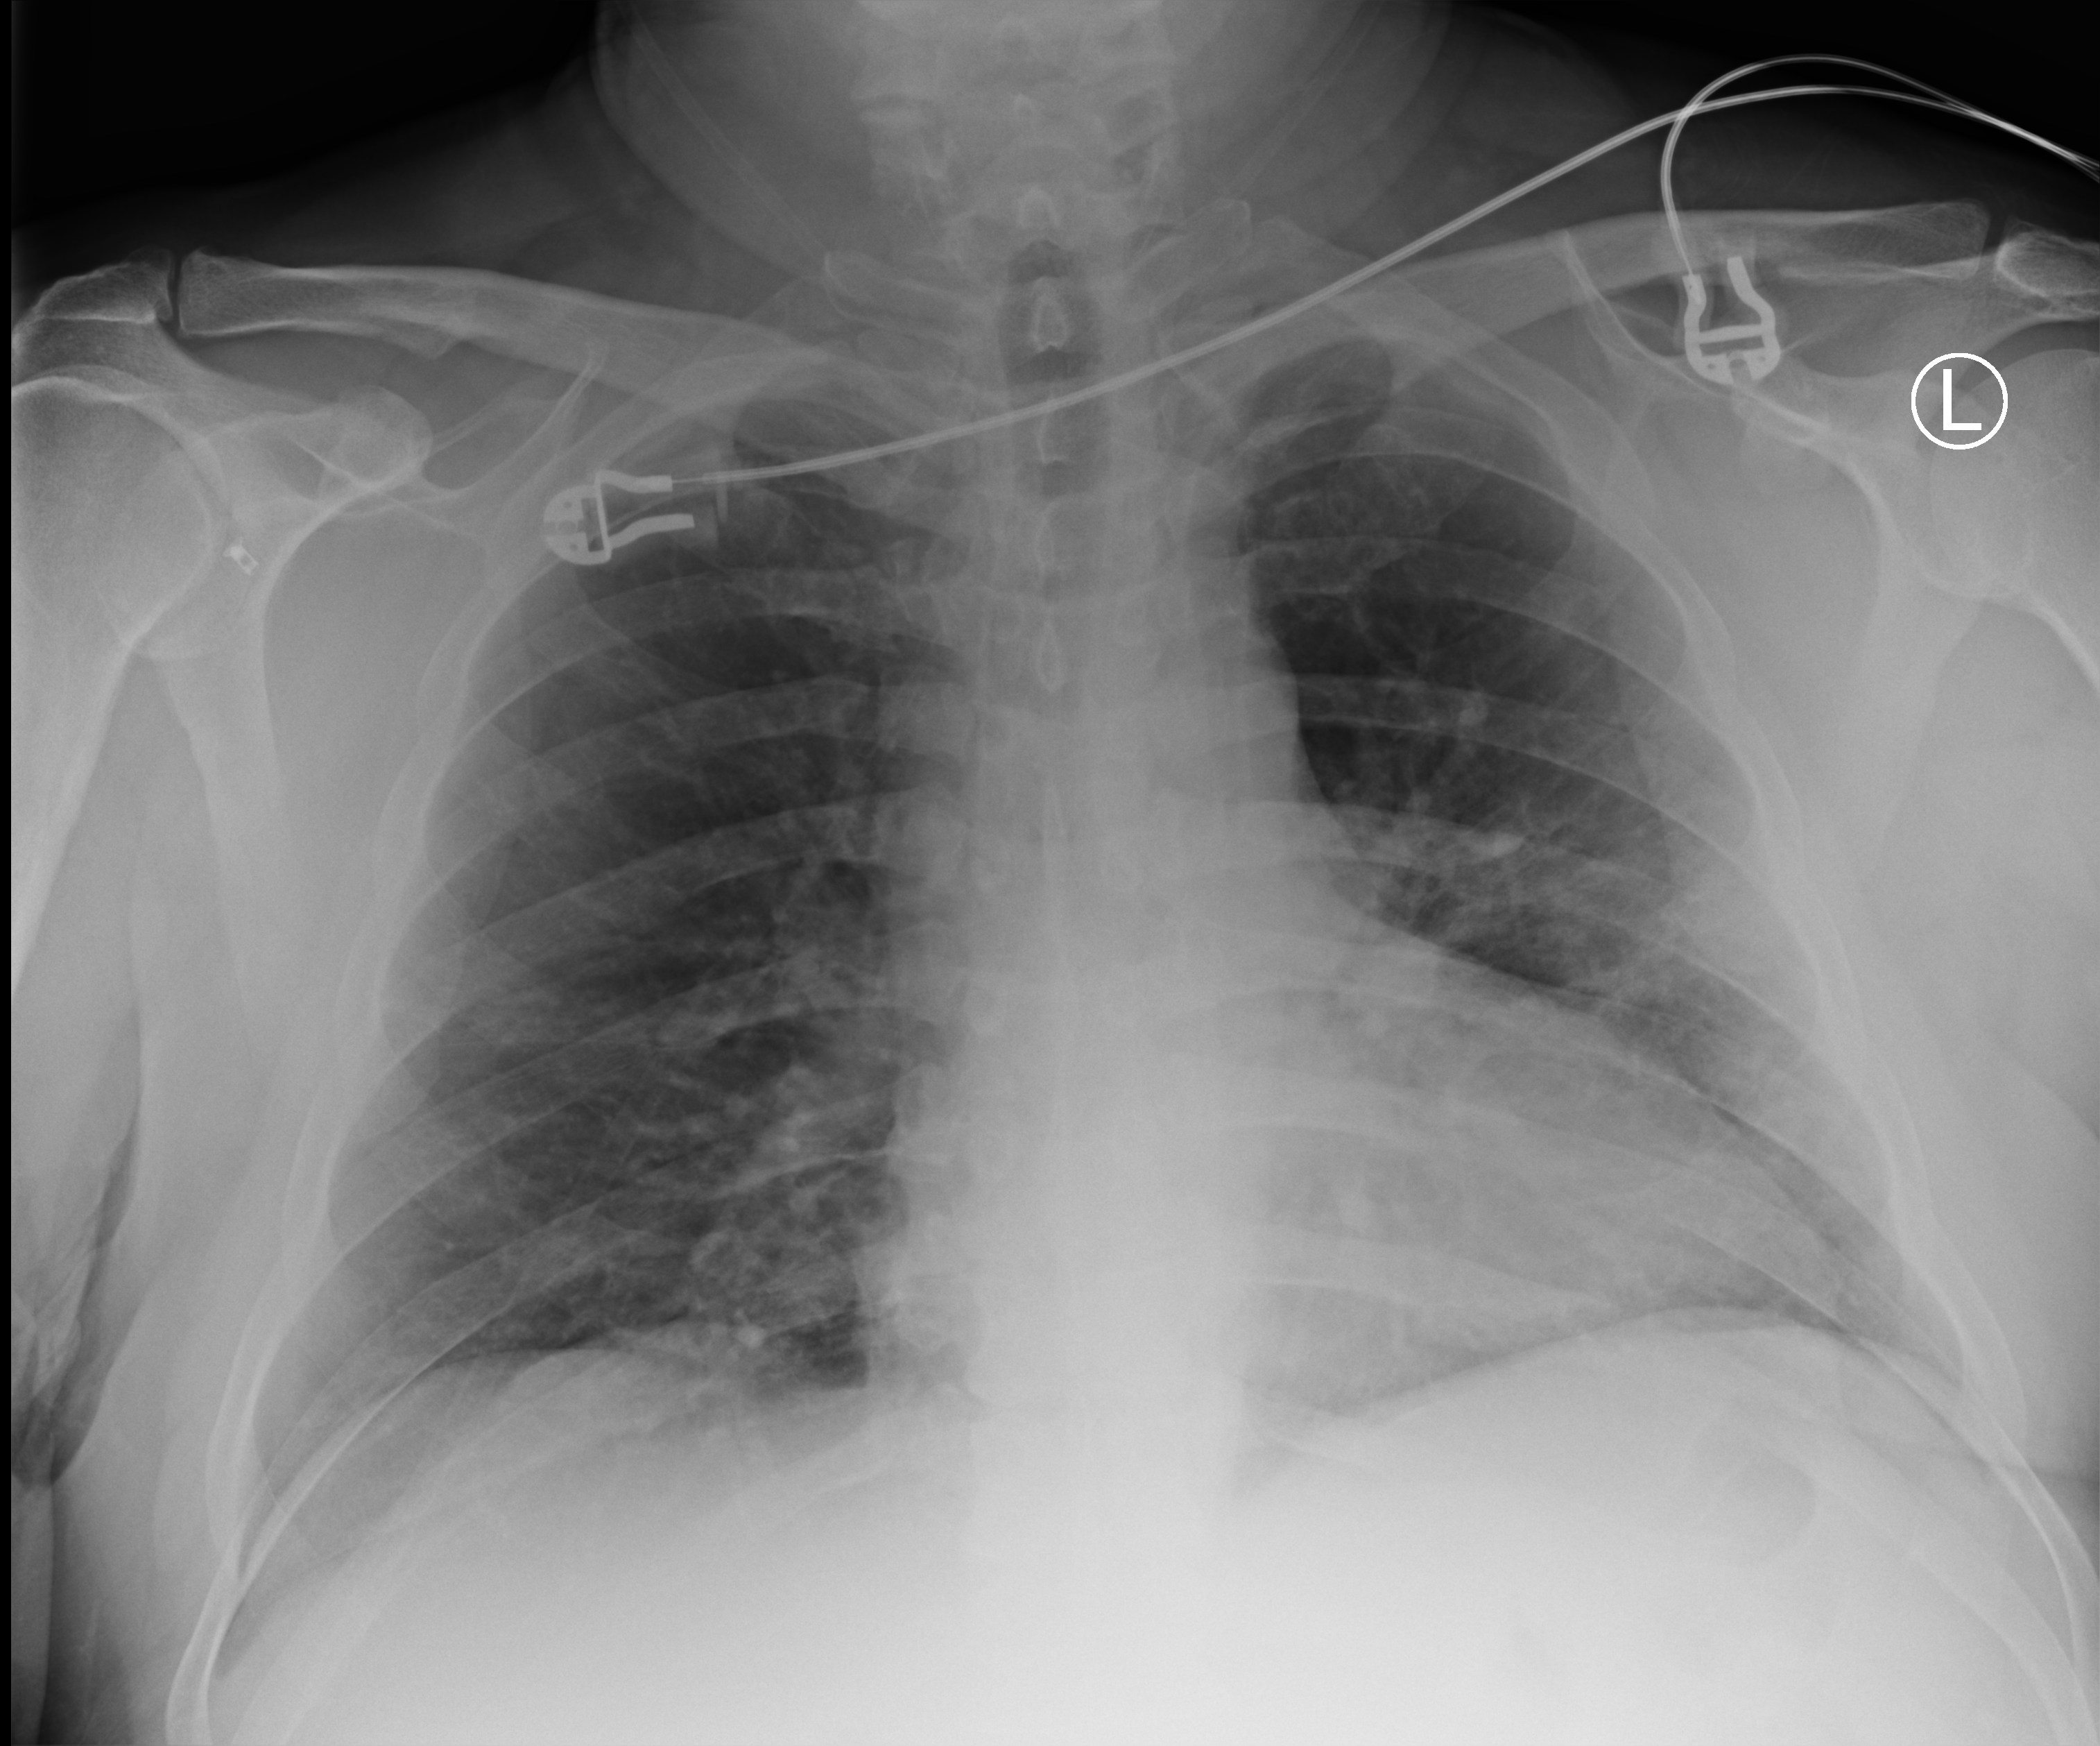
Bedside chest radiograph (computed radiography). Patient hospitalised with COVID-19; male, aged 18–59 years.
Admission-level facts for this patient (not findings on this image; timing relative to this image not recorded): admitted to intensive care during this hospital stay: yes; mechanically ventilated during this hospital stay: yes; diabetes (admission record): no.